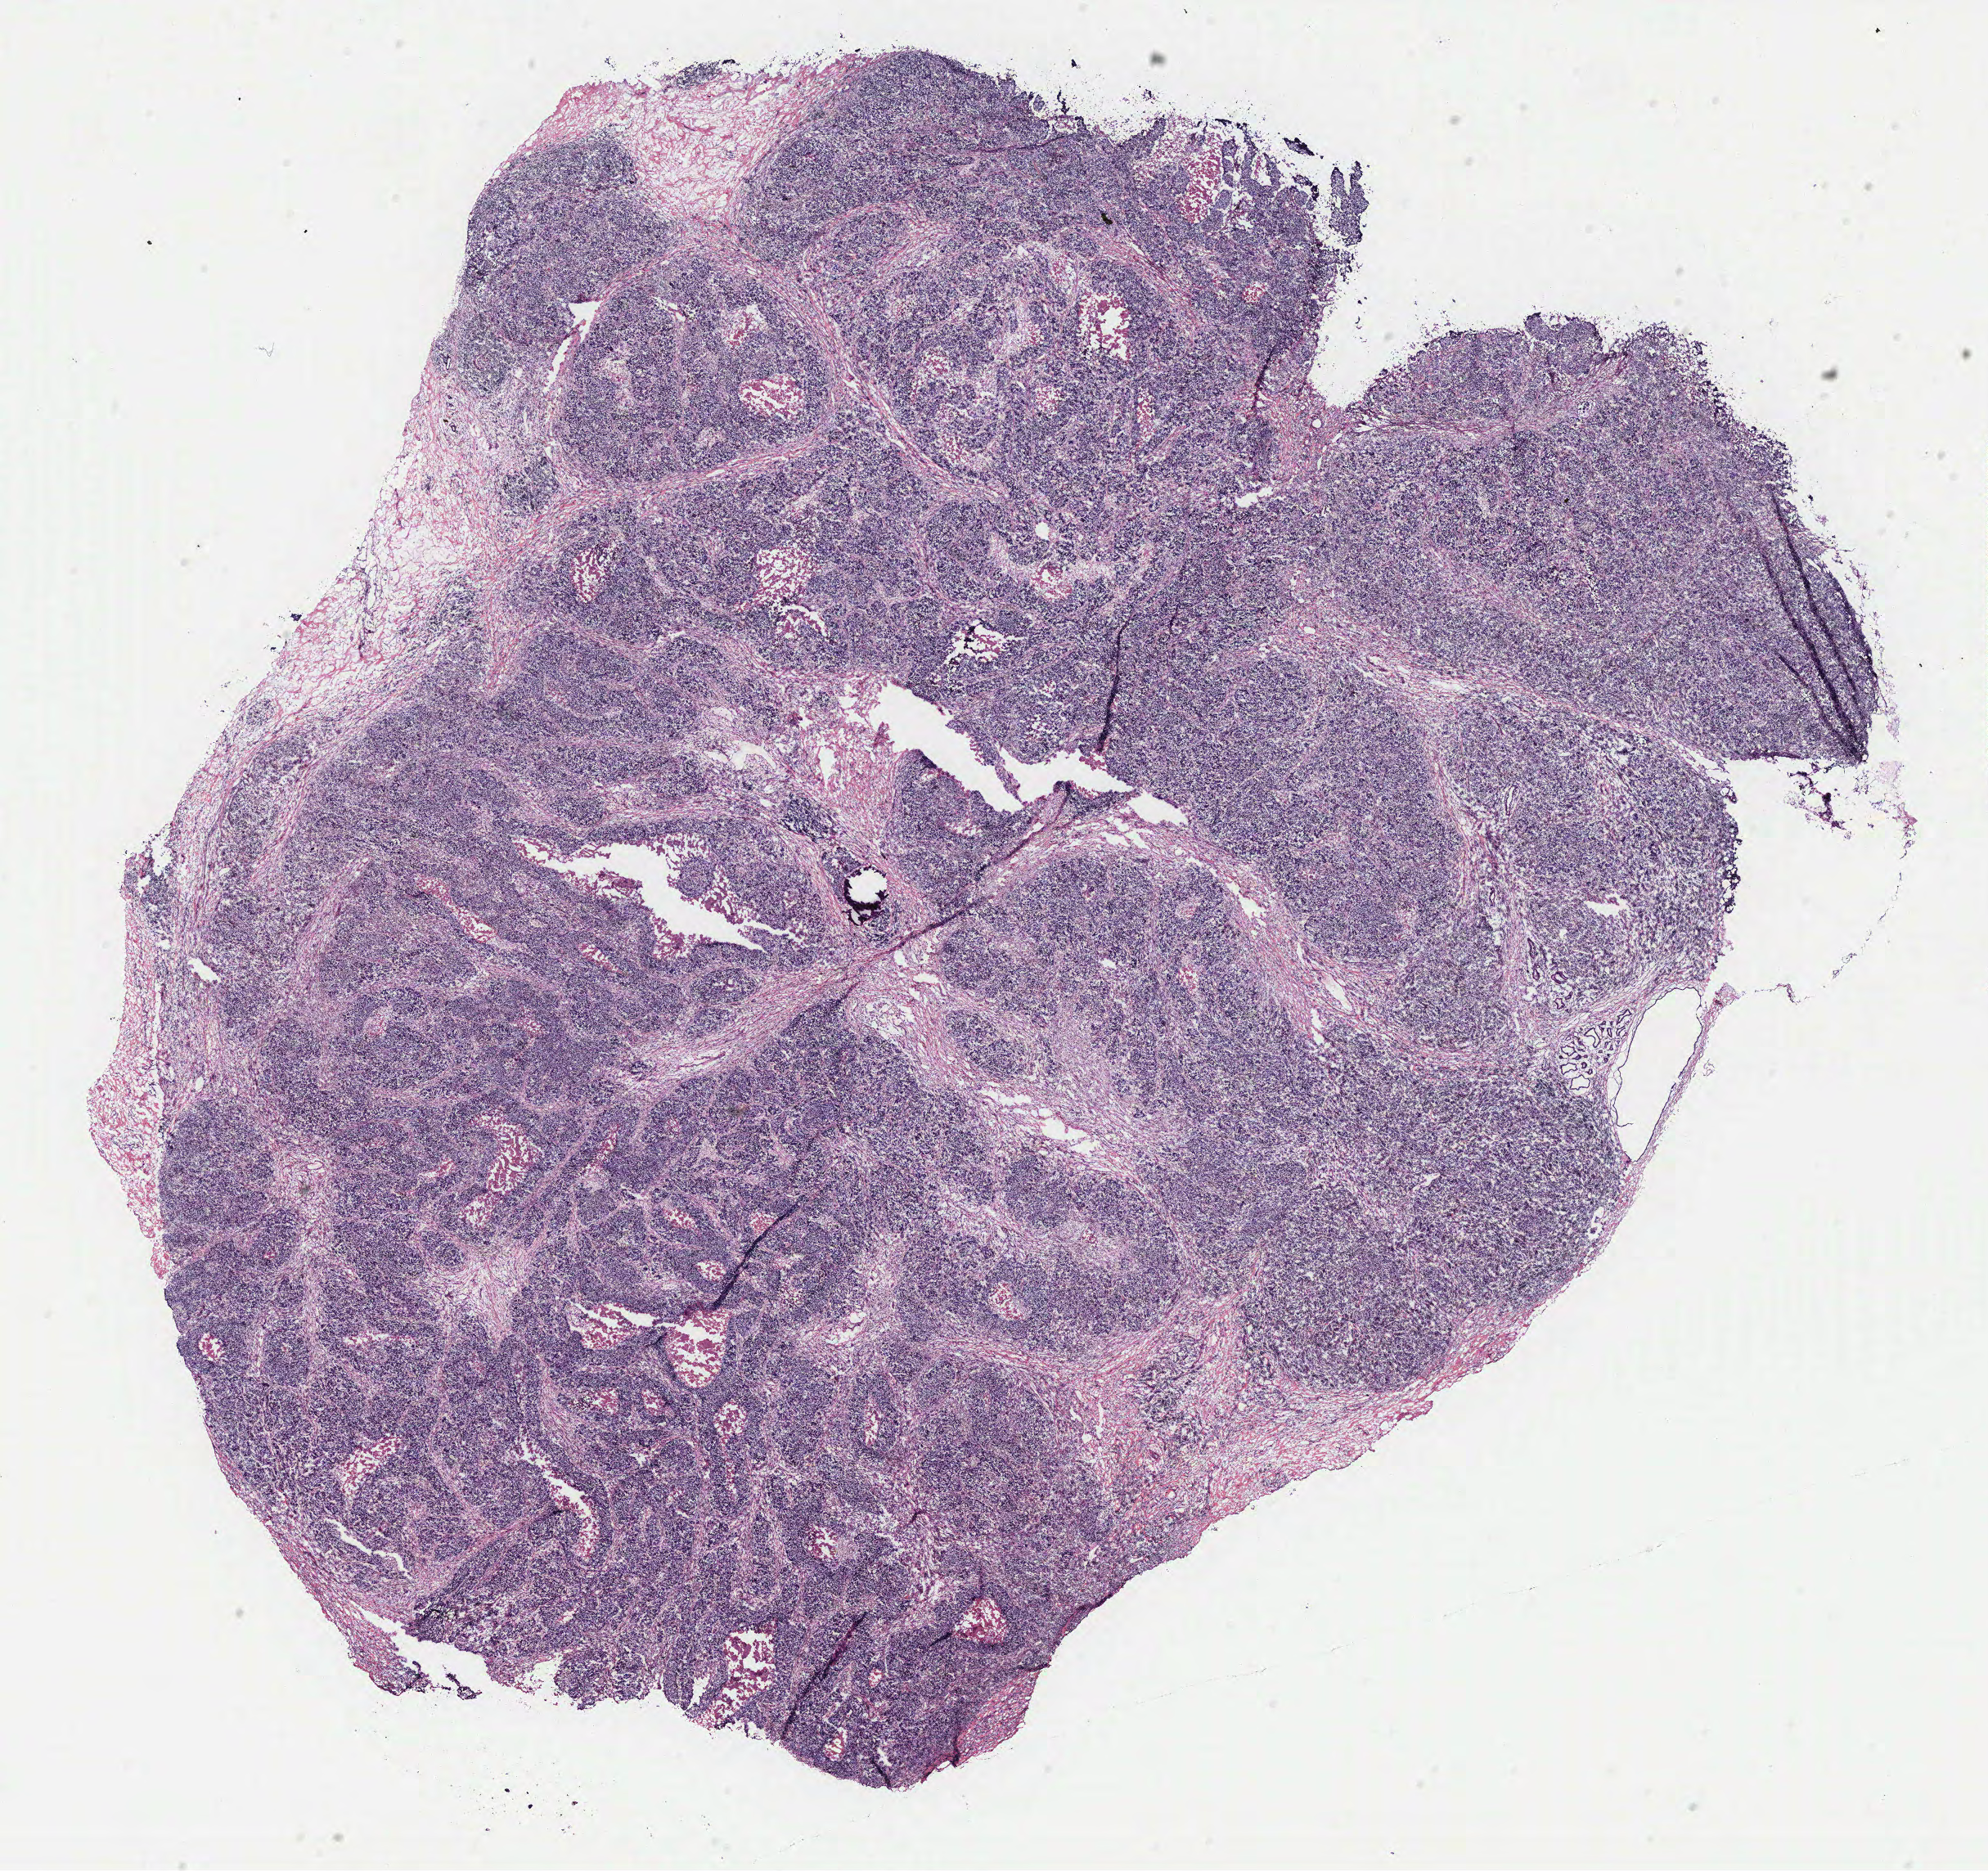
Digitized H&E-stained tissue section (whole slide), whole scanned area (about 19.4 x 18.3 mm, from a 40x scan) shown as a low-resolution overview, breast, tumour tissue. 53-year-old female patient.
AJCC pathologic stage: IIA. Diagnosis: Infiltrating duct carcinoma, NOS.